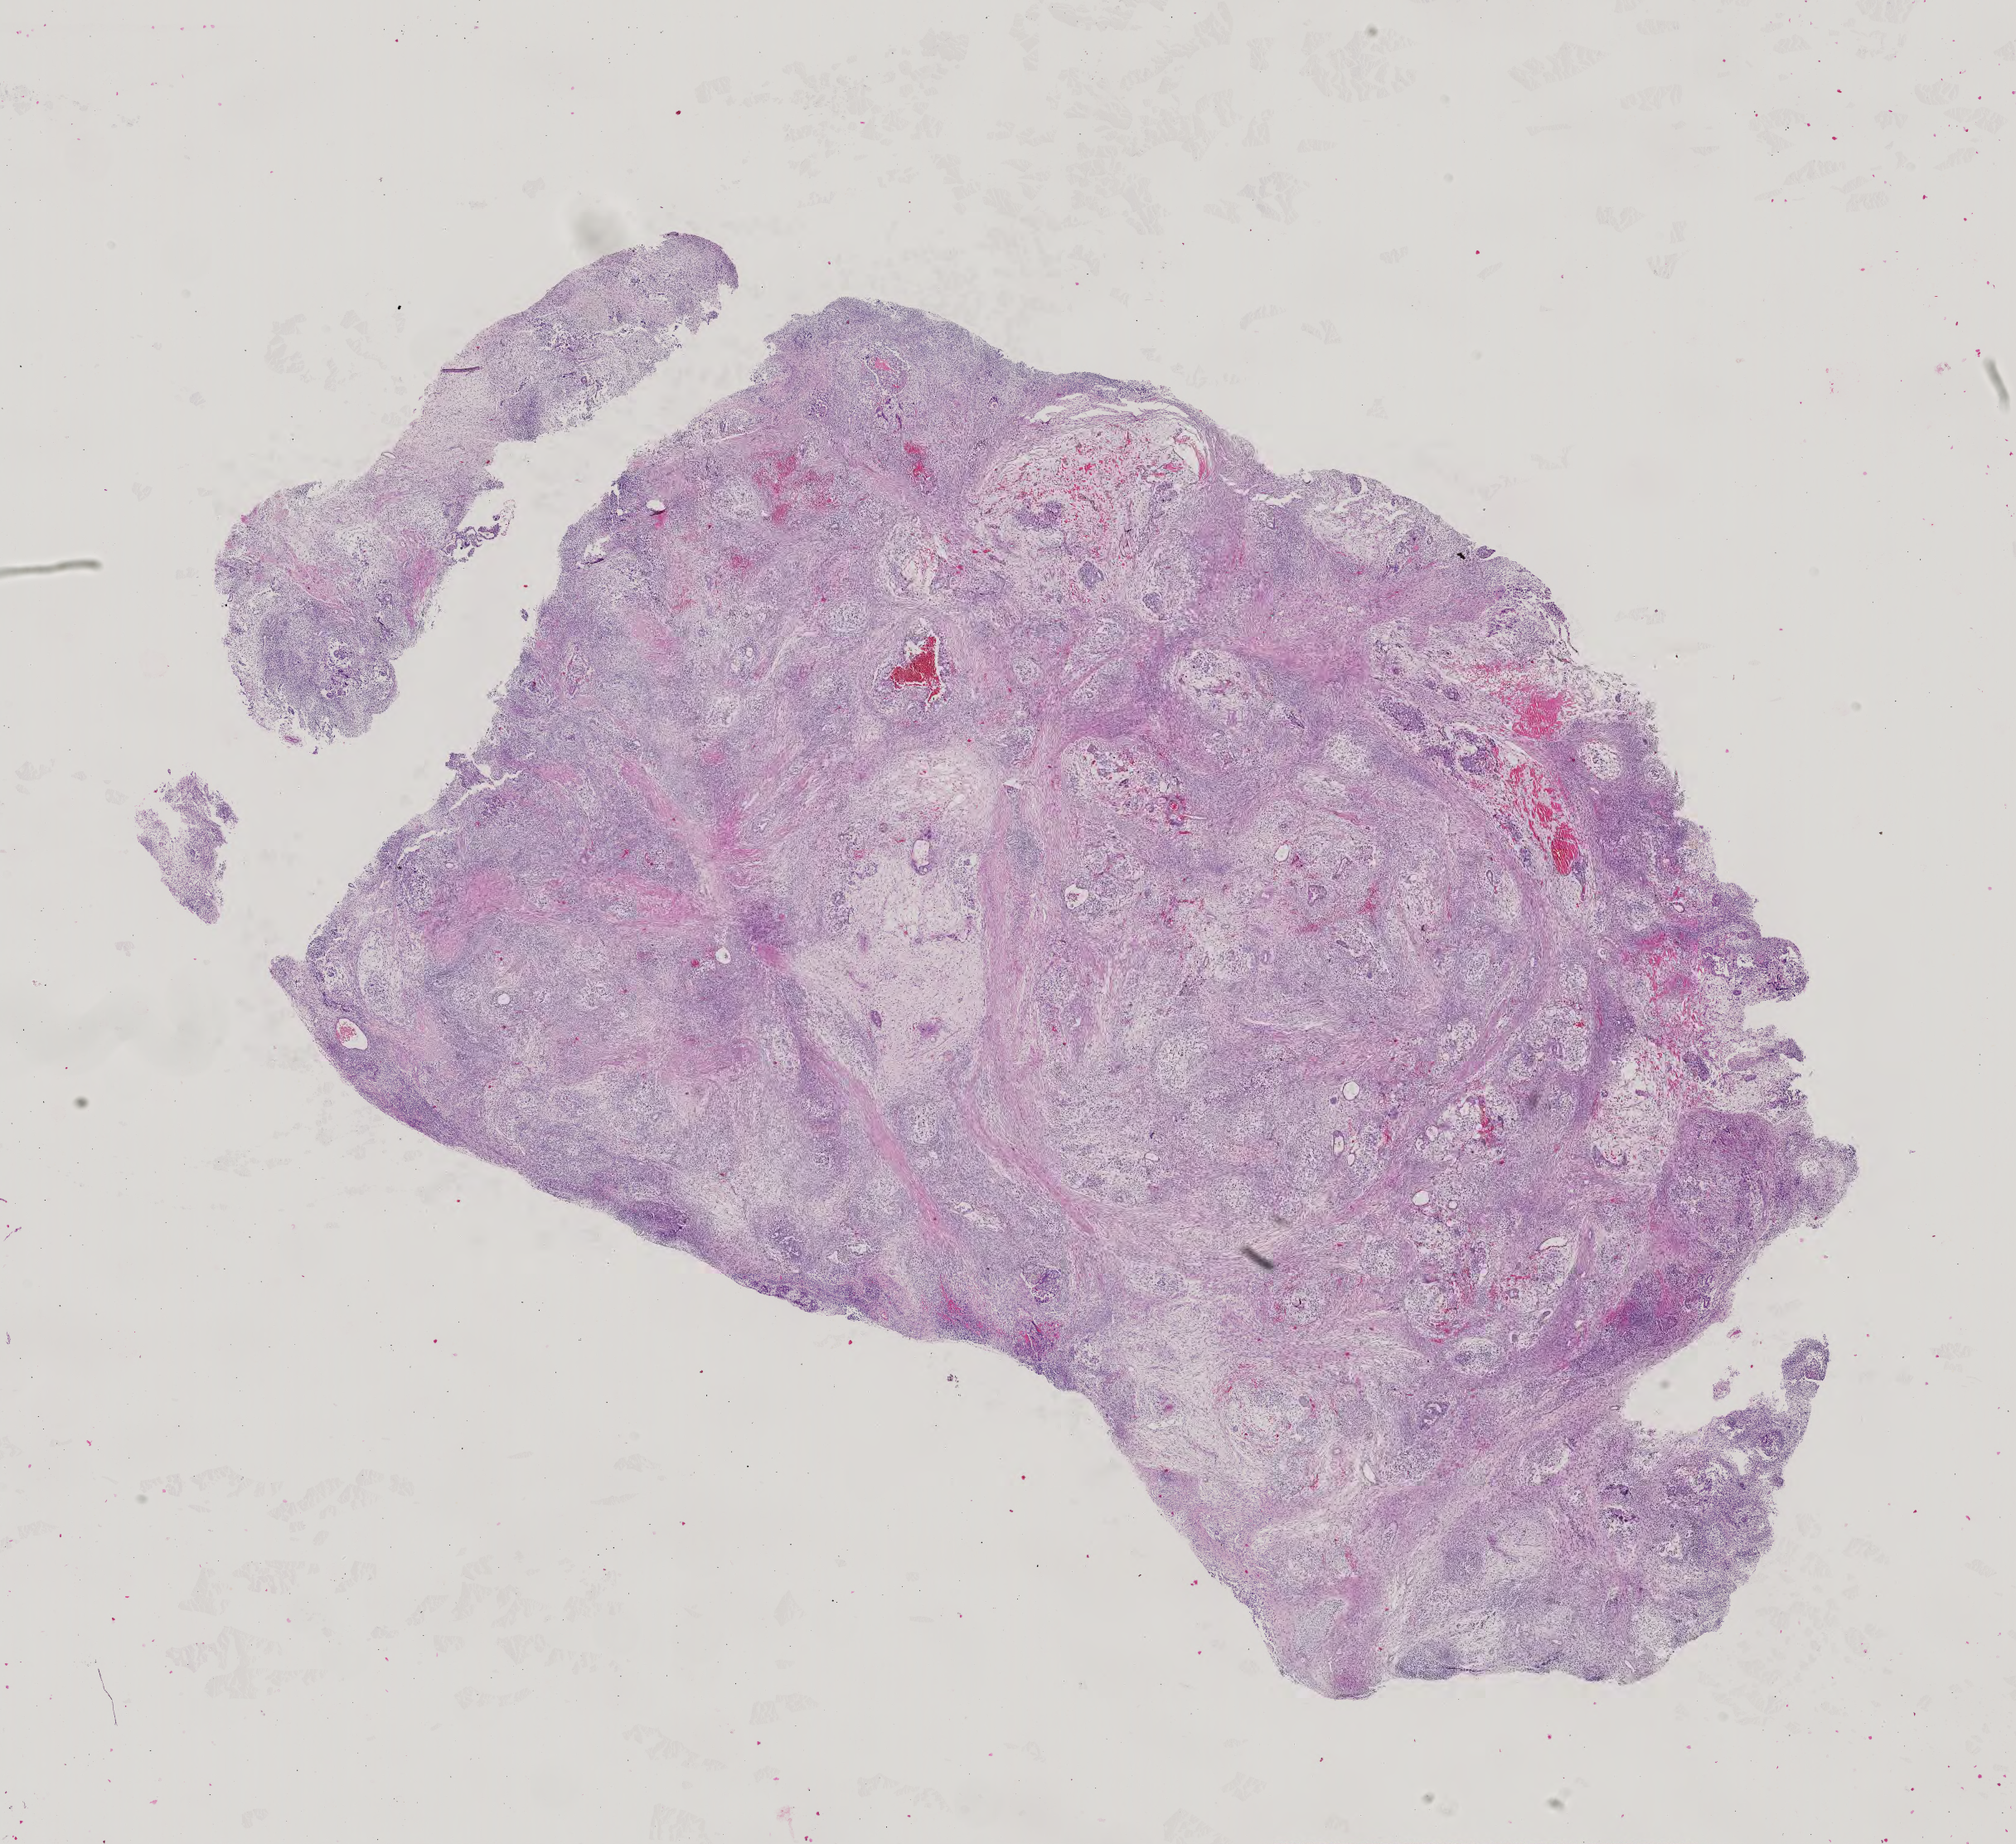
Whole-slide histology image, H&E — a low-resolution overview of the entire scanned area, about 17.7 x 16.2 mm (slide scanned at 40x), FFPE section, testis, primary tumour sample. Patient: male, age at initial diagnosis 20 years.
AJCC pathologic stage: IS (5th edition). Laterality: left. Pathologic diagnosis: Mixed germ cell tumor.